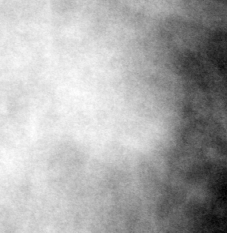
Cropped region of a digitized screen-film mammogram centred on a radiologist-marked abnormality; left breast; CC view; BI-RADS breast density category 3 (scale 1–4).
Mass, shape round, margins circumscribed; BI-RADS assessment category 4; subtlety rating 4 on a 1 (subtle) to 5 (obvious) scale; pathology result (as recorded, not read from the image): benign.